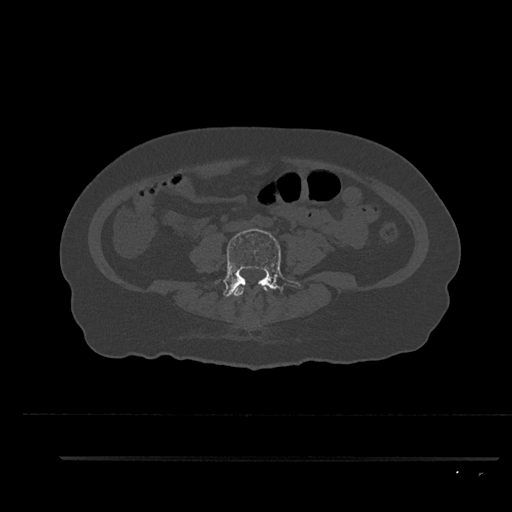
CT including the spine, one axial slice; position 34 of 797 along the scan axis; 120 kVp; bone window (W 1800 / L 400 HU); 0.5 mm slice thickness; 512 × 512 image matrix, field of view 408 × 408 mm. Female patient, age 44 years. Case-level facts recorded for this patient, not image findings: primary cancer: renal; vertebrae with lytic lesions (as recorded): L1.
Outlined on this slice (semi-automatically segmented with operator editing):
- L3 vertebra: bounding box <233,285,268,296> (left, top, right, bottom; pixels)
- L4 vertebra: <215,228,300,297>